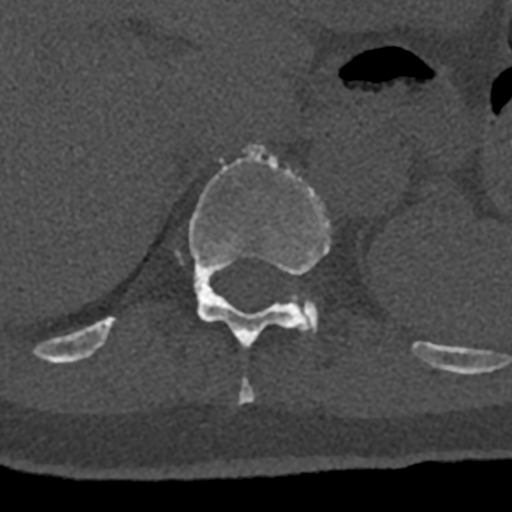
CT including the spine, one axial slice; slice 544 of 797 in the series (ordered by position); reconstruction kernel Br40s/3; 120 kVp; bone window (W 1800 / L 400 HU); 0.5 mm slice thickness; 512 × 512 image matrix, field of view 160 × 160 mm. Male patient, age 74 years. Case-level facts recorded for this patient, not image findings: primary cancer: renal.
Structures marked on this image (semi-automatic segmentation, software-assisted and operator-edited):
- T10 vertebra: bounding box [x1, y1, x2, y2] px = [238, 378, 255, 404]
- T11 vertebra: [70, 144, 432, 366]
- T12 vertebra: [292, 296, 318, 333]